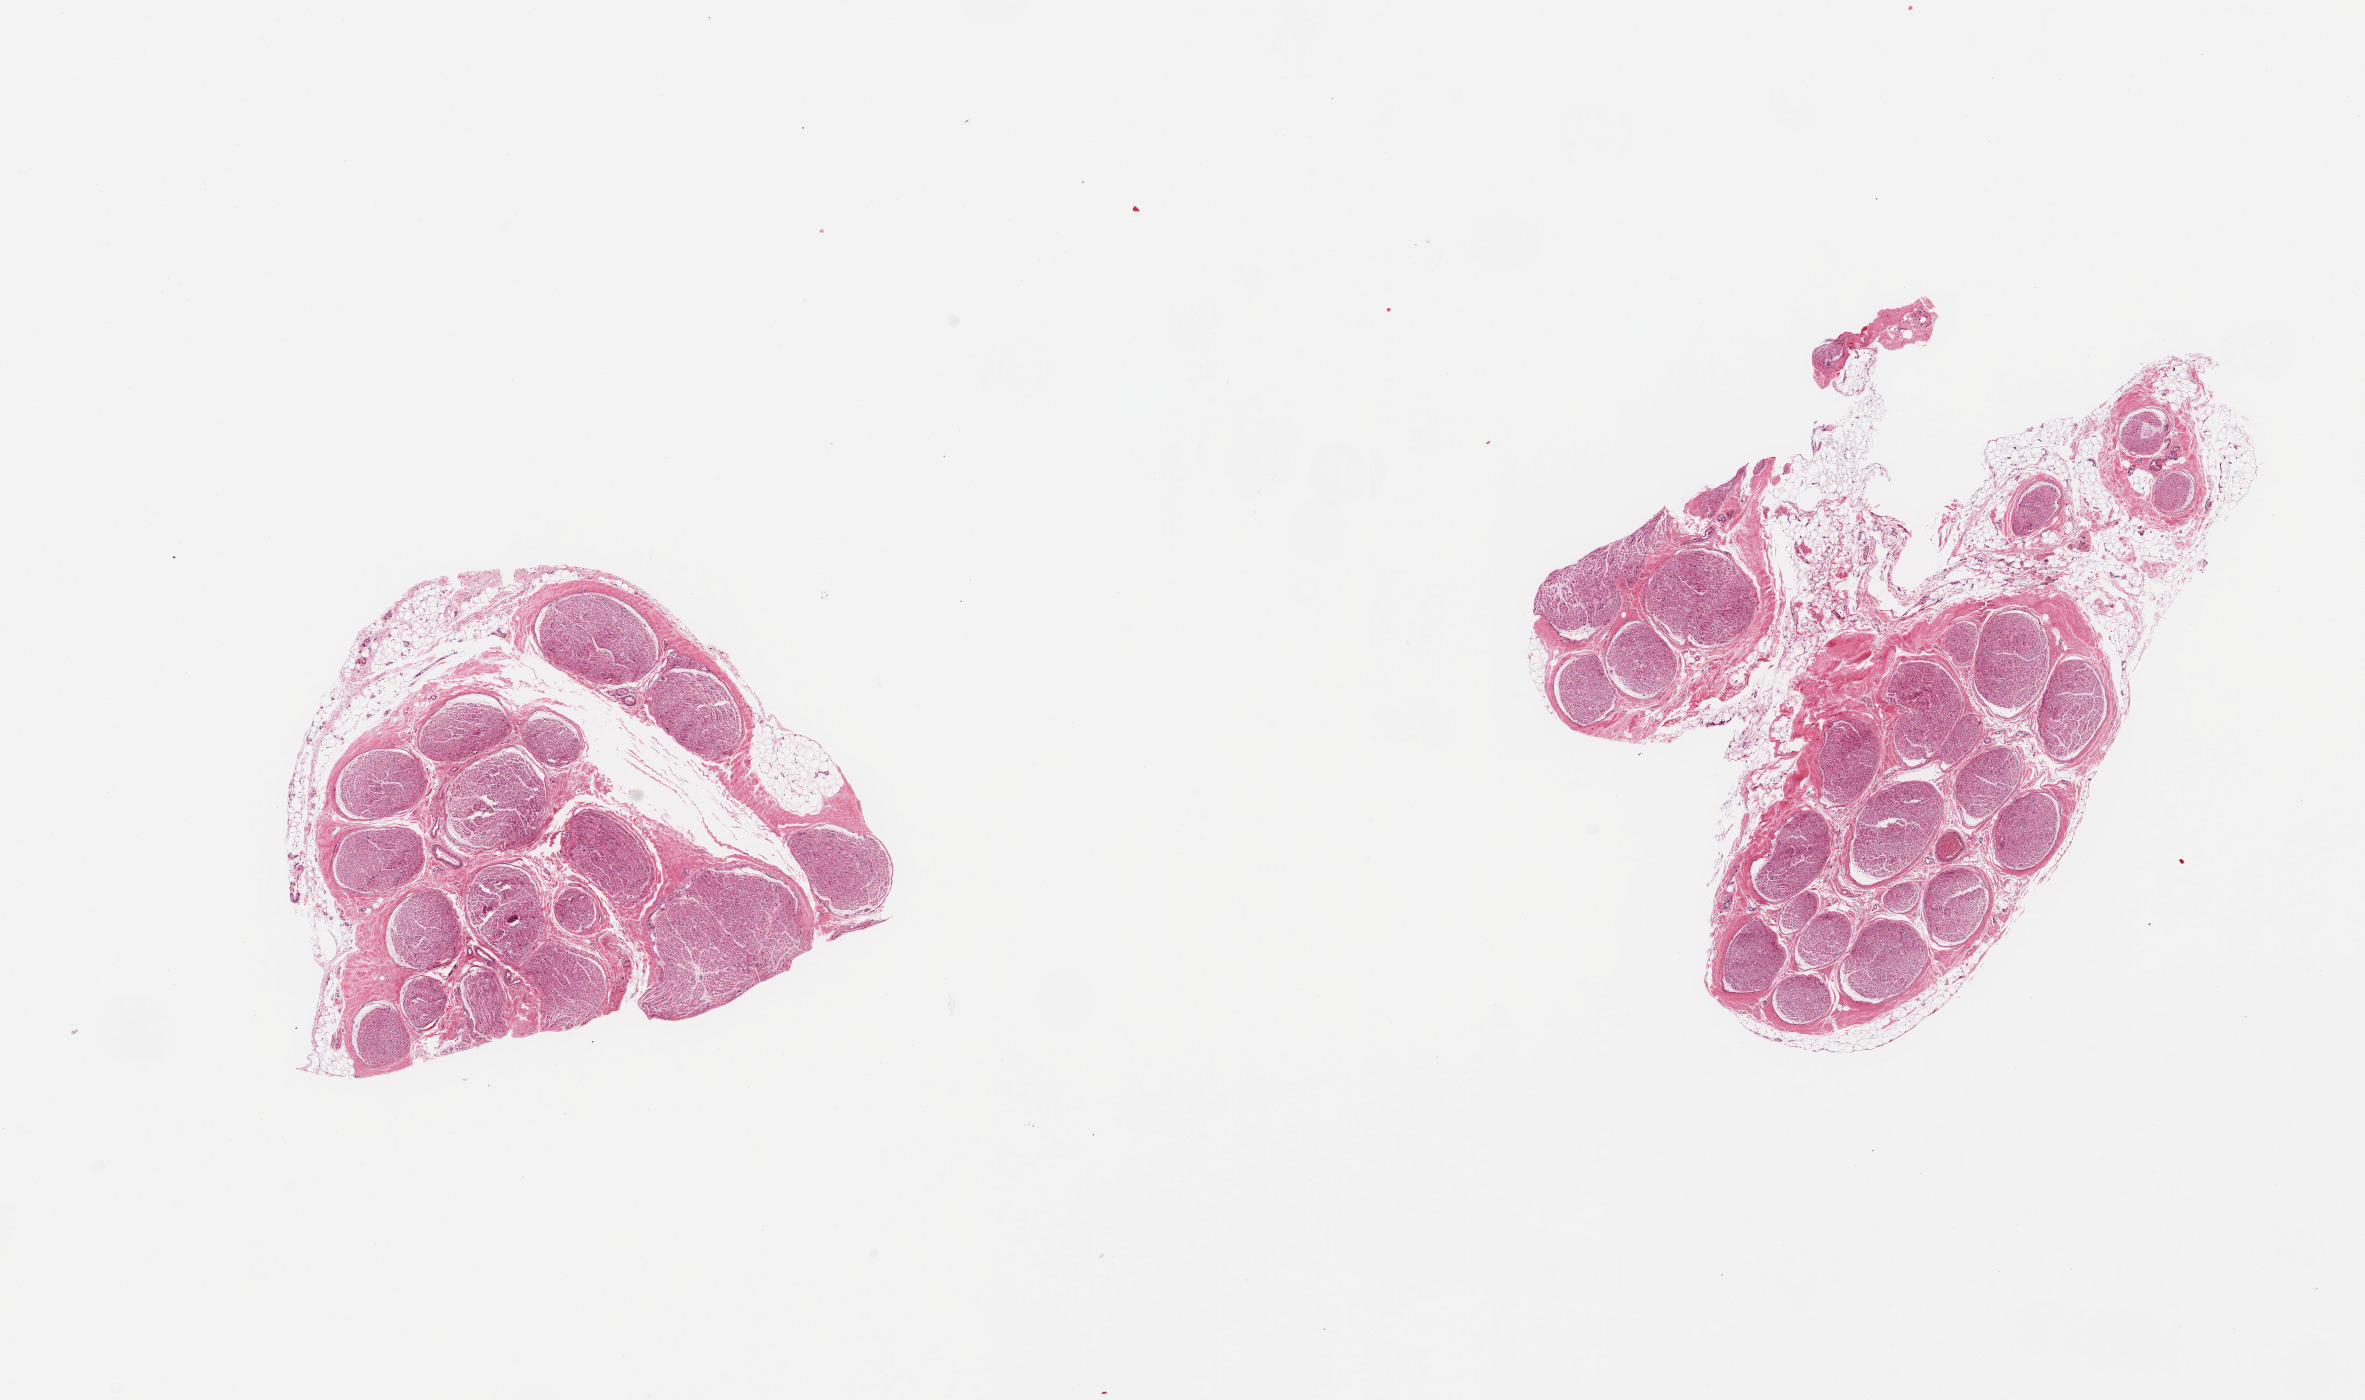
Digitized H&E-stained section, low-resolution overview of the scanned area, about 18.7 x 11.1 mm (acquisition: 20x scan), PAXgene-fixed, paraffin-embedded tissue, sampled site (target tissue): tibial nerve, tissue donor sample.
Pathologist's review note for this sample: 2 pieces; 10 & 20% internal & external fat.